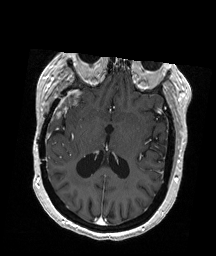
Brain MRI from a brain-tumour surgery series, one axial slice. Slice 98 of 192 in the series (ordered by position). T1-weighted post-contrast. 1 mm slice thickness. 216 × 256 image matrix. From the clinical record (not read from this slice): histopathology: Glioblastoma; WHO grade: 4; IDH mutation: no; tumour location: Right Temporal.
Outlined on this slice (outlined manually by an expert reader):
- tumour: bounding box [x1, y1, x2, y2] px = [57, 91, 81, 115]